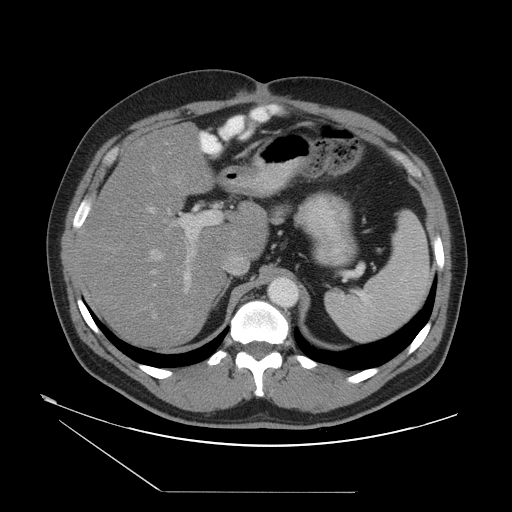
Contrast-enhanced abdominal CT, one axial slice. Position 32 of 55 along the scan axis. 120 kVp. Soft-tissue window (W 400 / L 40 HU). 512 × 512 image matrix. Male patient, age 59 years. Case-level facts recorded for this patient, not image findings: diagnosis: colorectal cancer liver metastases, imaged before liver resection; multiple liver metastases: yes; largest metastasis: 0.3 cm; chemotherapy before resection: yes.
Structures marked on this image (outlined manually by an expert reader):
- hepatic veins: bounding box (x1, y1, x2, y2) in pixels: (149, 136, 235, 319)
- liver: (81, 125, 266, 346)
- planned liver remnant (the part of the liver to remain after resection): (81, 142, 265, 346)
- portal vein (with intrahepatic branches): (147, 143, 223, 294)